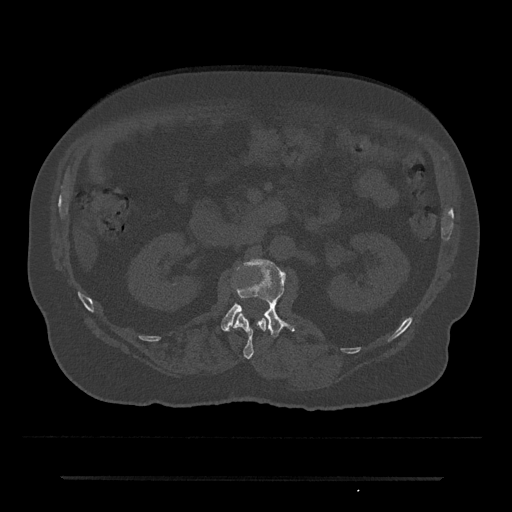
CT including the spine, one axial slice; slice 34 of 797 in the series (ordered by position); 120 kVp; bone window (W 1800 / L 400 HU); 0.5 mm slice thickness; 512 × 512 image matrix. Male patient, age 69 years. From the clinical record (not read from this slice): primary cancer: prostate.
Outlined on this slice (semi-automatic segmentation, software-assisted and operator-edited):
- L1 vertebra: bounding box <233,313,267,359> (left, top, right, bottom; pixels)
- L2 vertebra: <221,259,295,337>